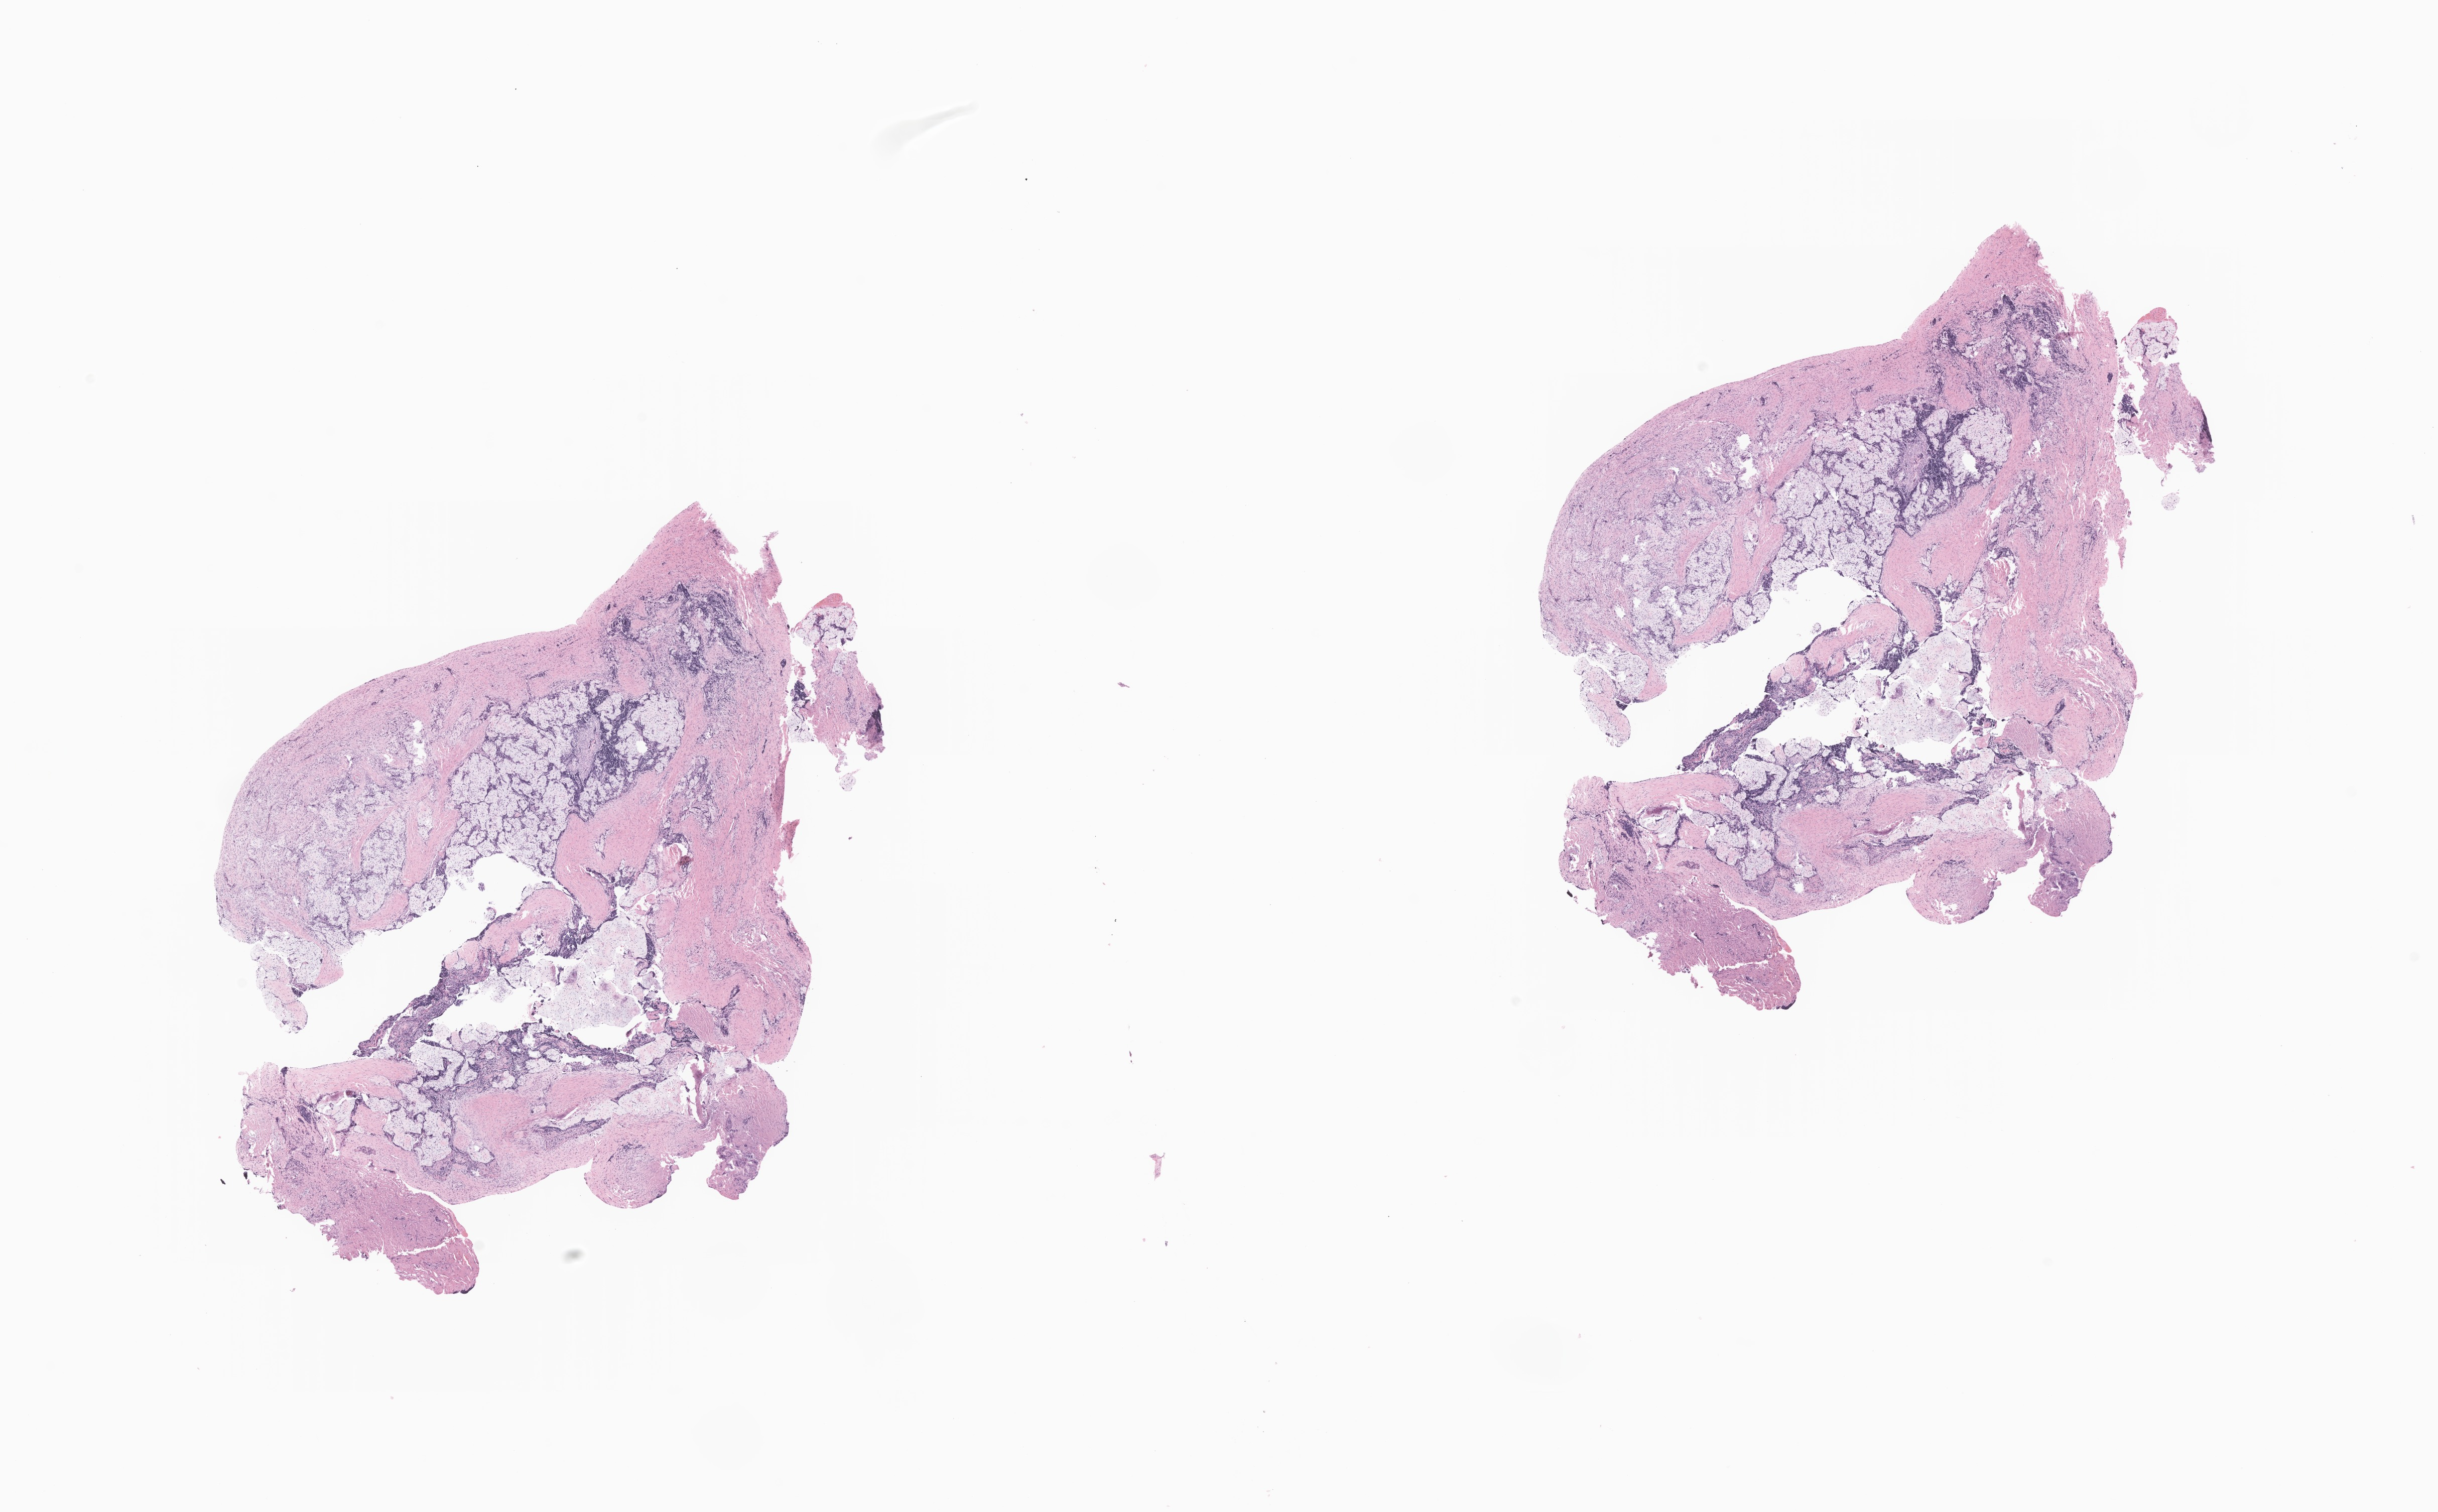
Digitized H&E-stained section of tumor tissue from the spinal cord — a low-resolution overview of the entire scanned area, about 20.5 x 12.7 mm, formalin-fixed paraffin-embedded section. Patient male; age 146 months (12 years 2 months).
* recorded diagnosis: Mesenchymal chondrosarcoma